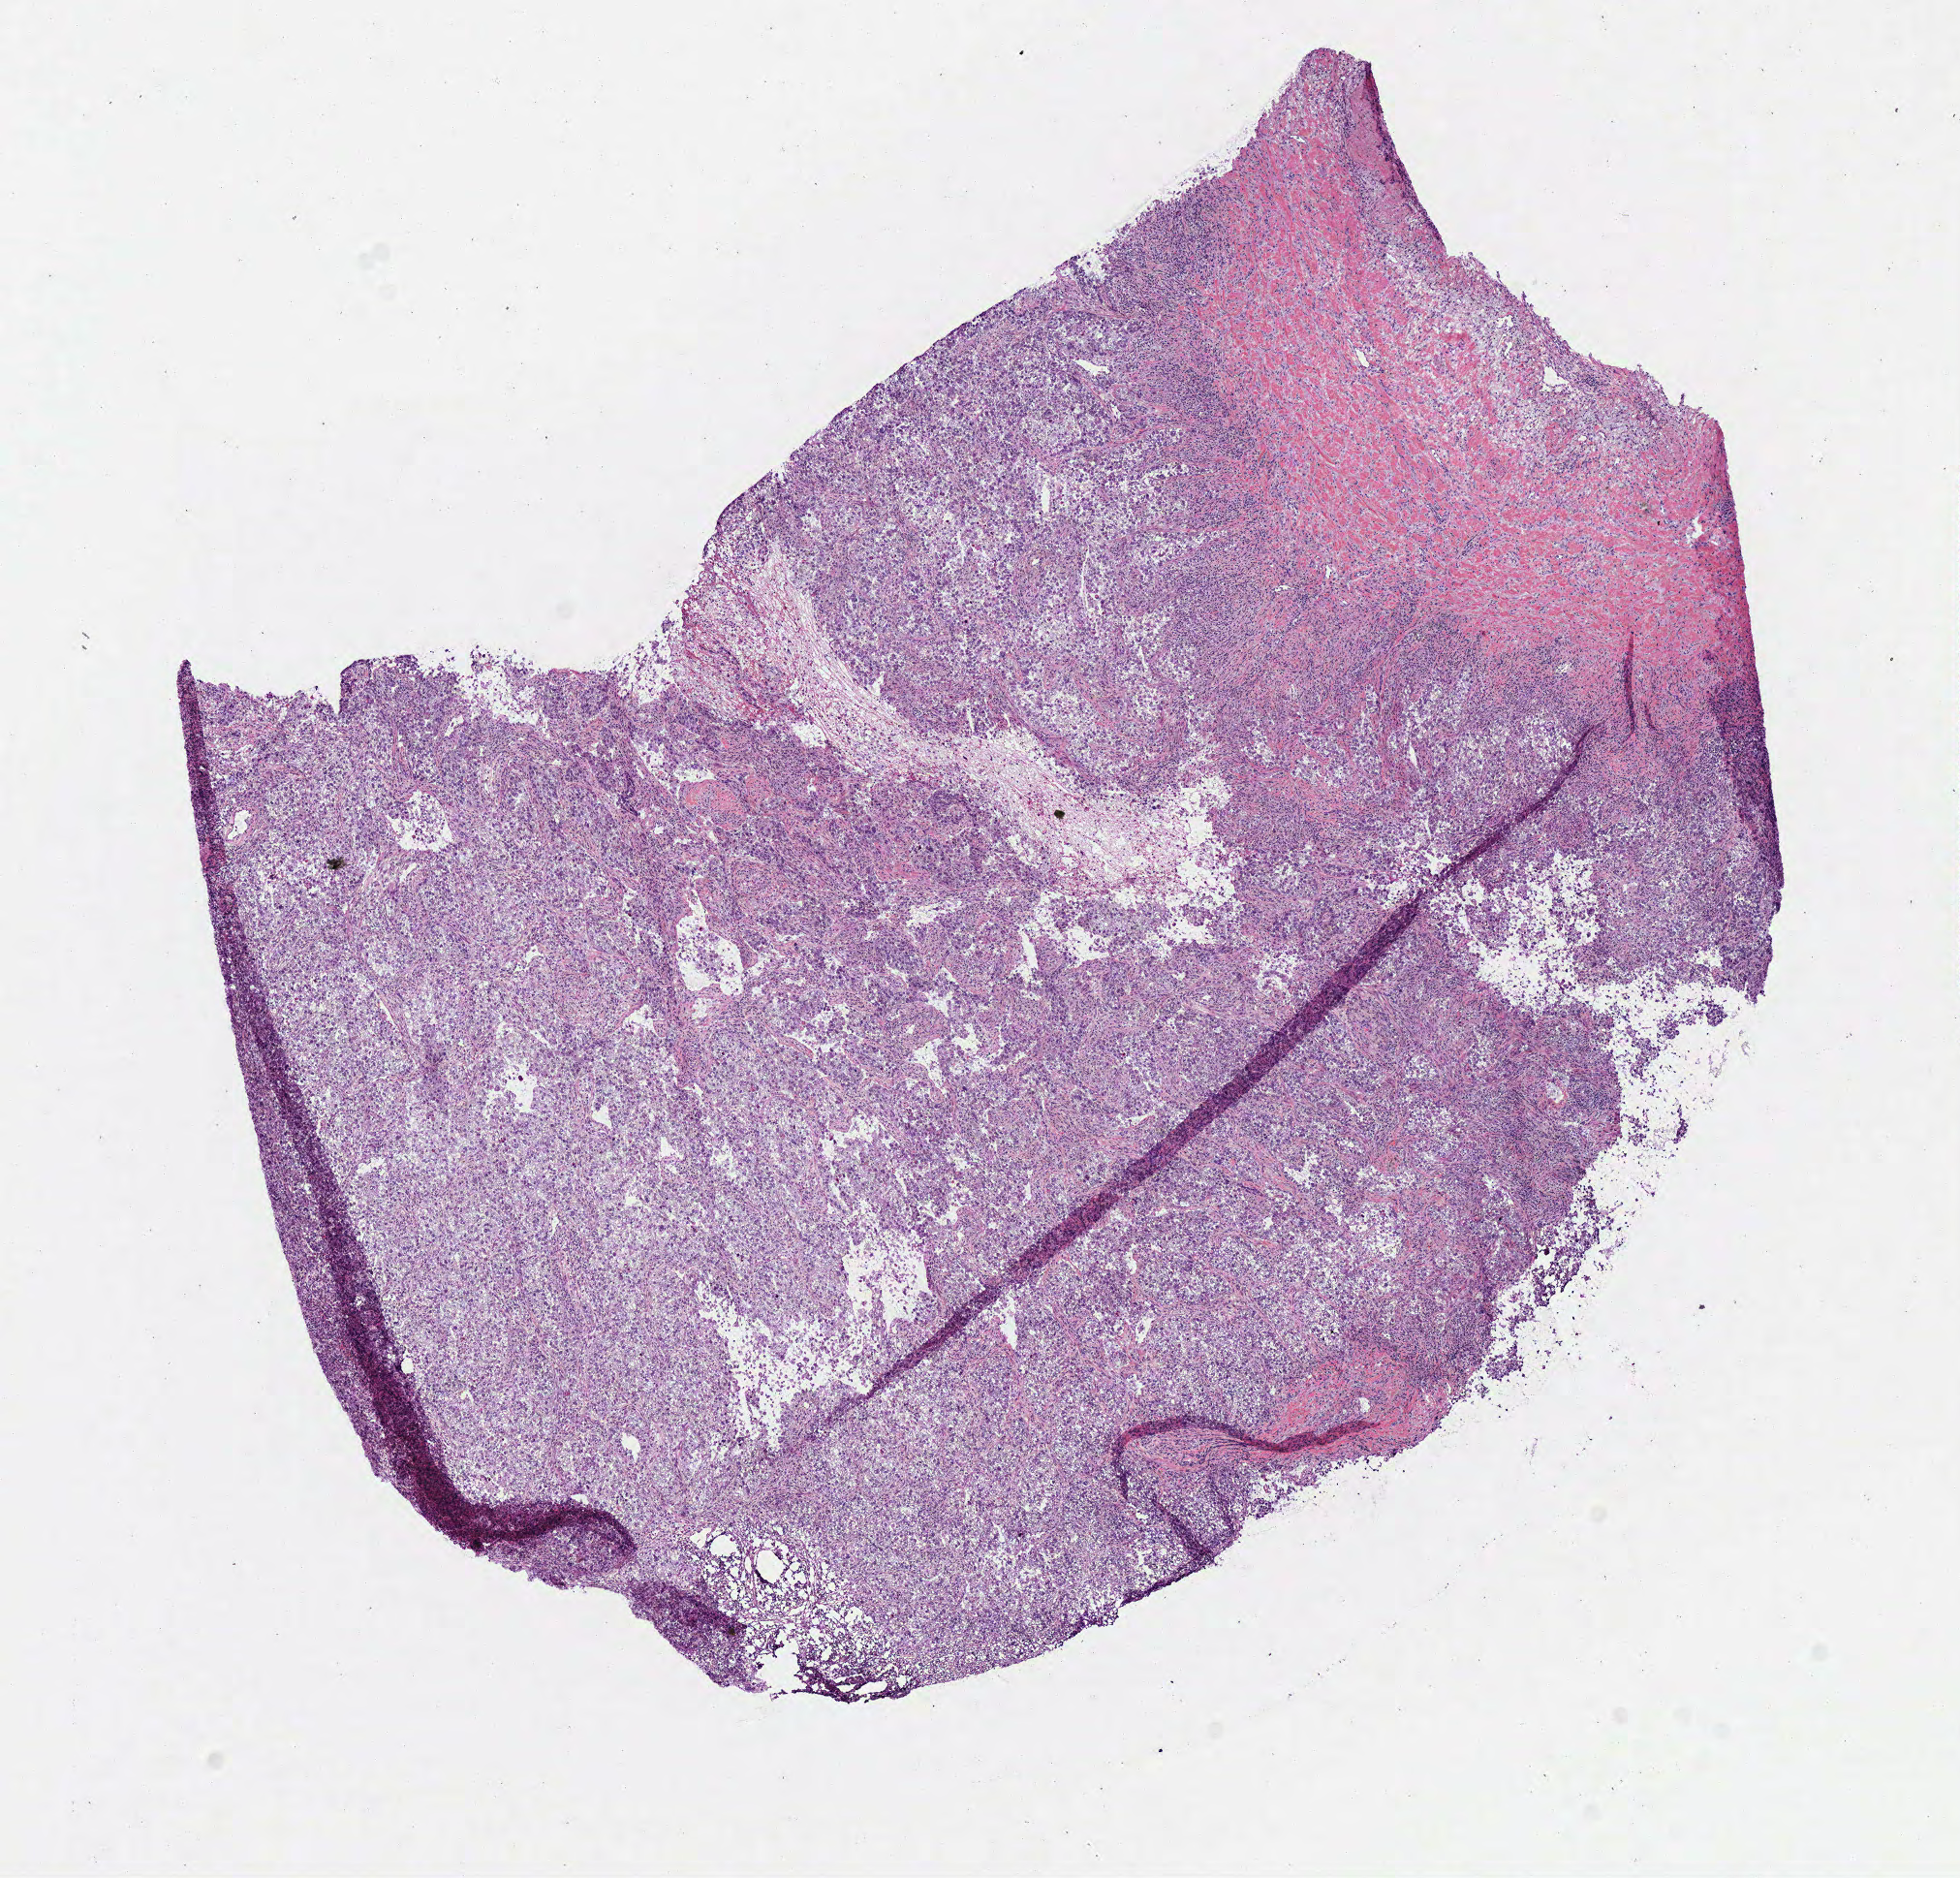
Digitized H&E tissue section (whole slide) — whole scanned area (about 8.0 x 7.6 mm) shown as a low-resolution overview. Frozen section from the bottom of the tissue portion. Lung, primary tumour sample. Male patient. Slide review estimates, as recorded: tumour cells 85%, tumour nuclei 80%, normal cells 0%, stromal cells 15%, necrosis 0%. Infiltration values recorded for this section: lymphocyte infiltration 10%, monocyte infiltration 2%, neutrophil infiltration 2%.
AJCC pathologic stage: IIA (6th edition). Histologic diagnosis: Squamous cell carcinoma, NOS.